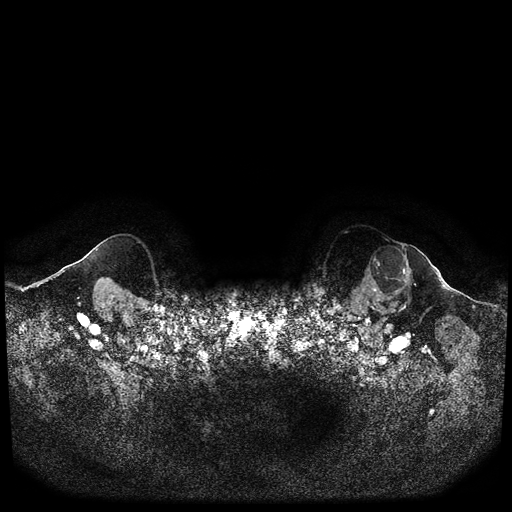
Breast MRI (dynamic contrast-enhanced, multi-phase), one axial slice; position 100 of 116 along the scan axis; dynamic contrast-enhanced series, time point 2 of 5 at this slice position (early post-contrast); 1.5 T; TE 2.6 ms, TR 5.3 ms; 2 mm slice thickness; 512 × 512 image matrix, field of view 350 × 350 mm. Patient: female, 64 years.
Outlined on this slice (semi-automatically segmented with operator editing):
- breast lesion (labelled 'tumour' in the annotation; benign lesions carry a separate 'benign' label): bounding box <361,245,414,302> (left, top, right, bottom; pixels)